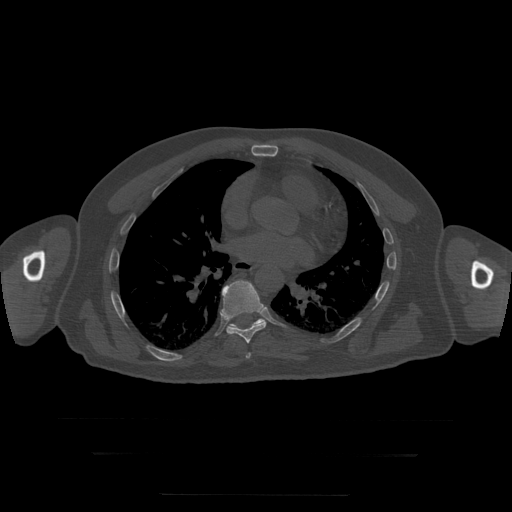
CT including the spine, one axial slice; position 162 of 397 along the scan axis; reconstruction kernel STANDARD; bone window (W 1800 / L 400 HU); 1.25 mm slice thickness; 512 × 512 image matrix, field of view 510 × 510 mm. Patient age 73 years. From the clinical record (not read from this slice): primary cancer: prostate.
Outlined on this slice (semi-automatic segmentation, software-assisted and operator-edited):
- T7 vertebra: box from (x=246, y=353) to (x=251, y=359) px
- T8 vertebra: (x=221, y=281)–(x=267, y=344)
- T9 vertebra: (x=230, y=319)–(x=265, y=328)